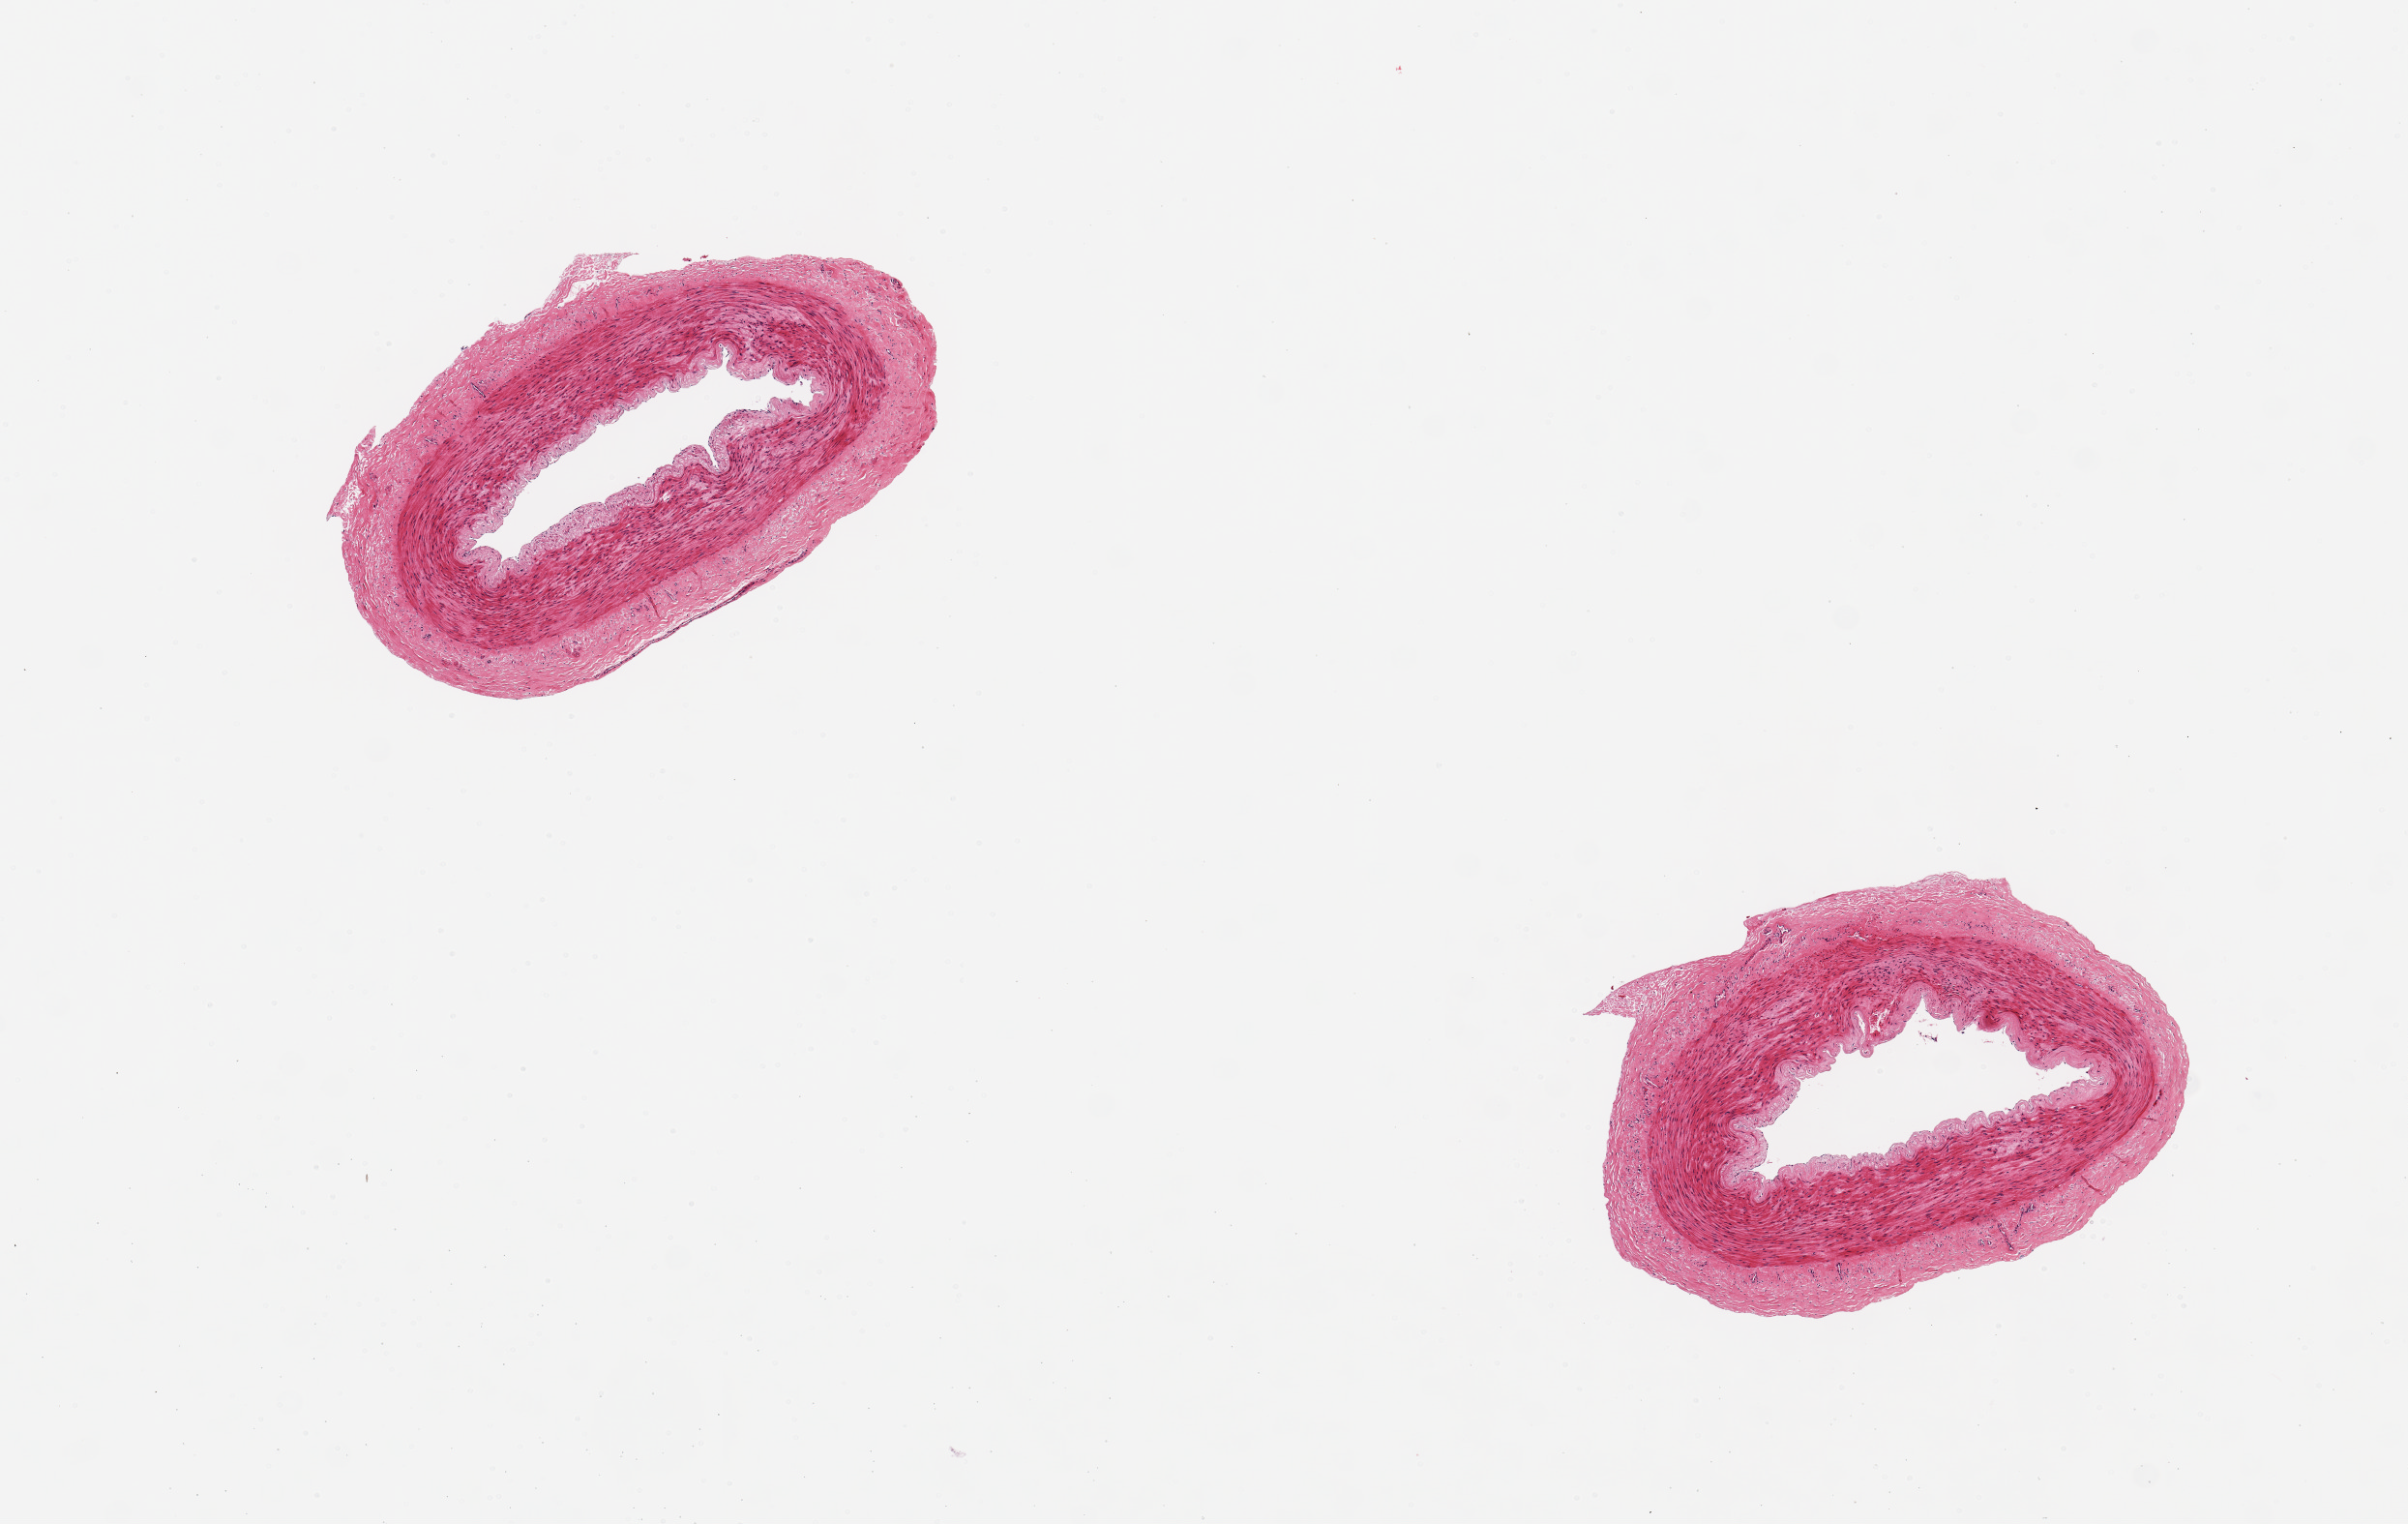
Digitized hematoxylin and eosin (H&E)-stained section — low-resolution overview of the scanned area, about 9.8 x 6.2 mm (acquisition: 20x scan), PAXgene-fixed, paraffin-embedded tissue, sampled site (target tissue): tibial artery, donor tissue sample. Donor: male.
Reviewer comment on this tissue sample: 2 aliquots, 2.5mm d. Good clean specimens.